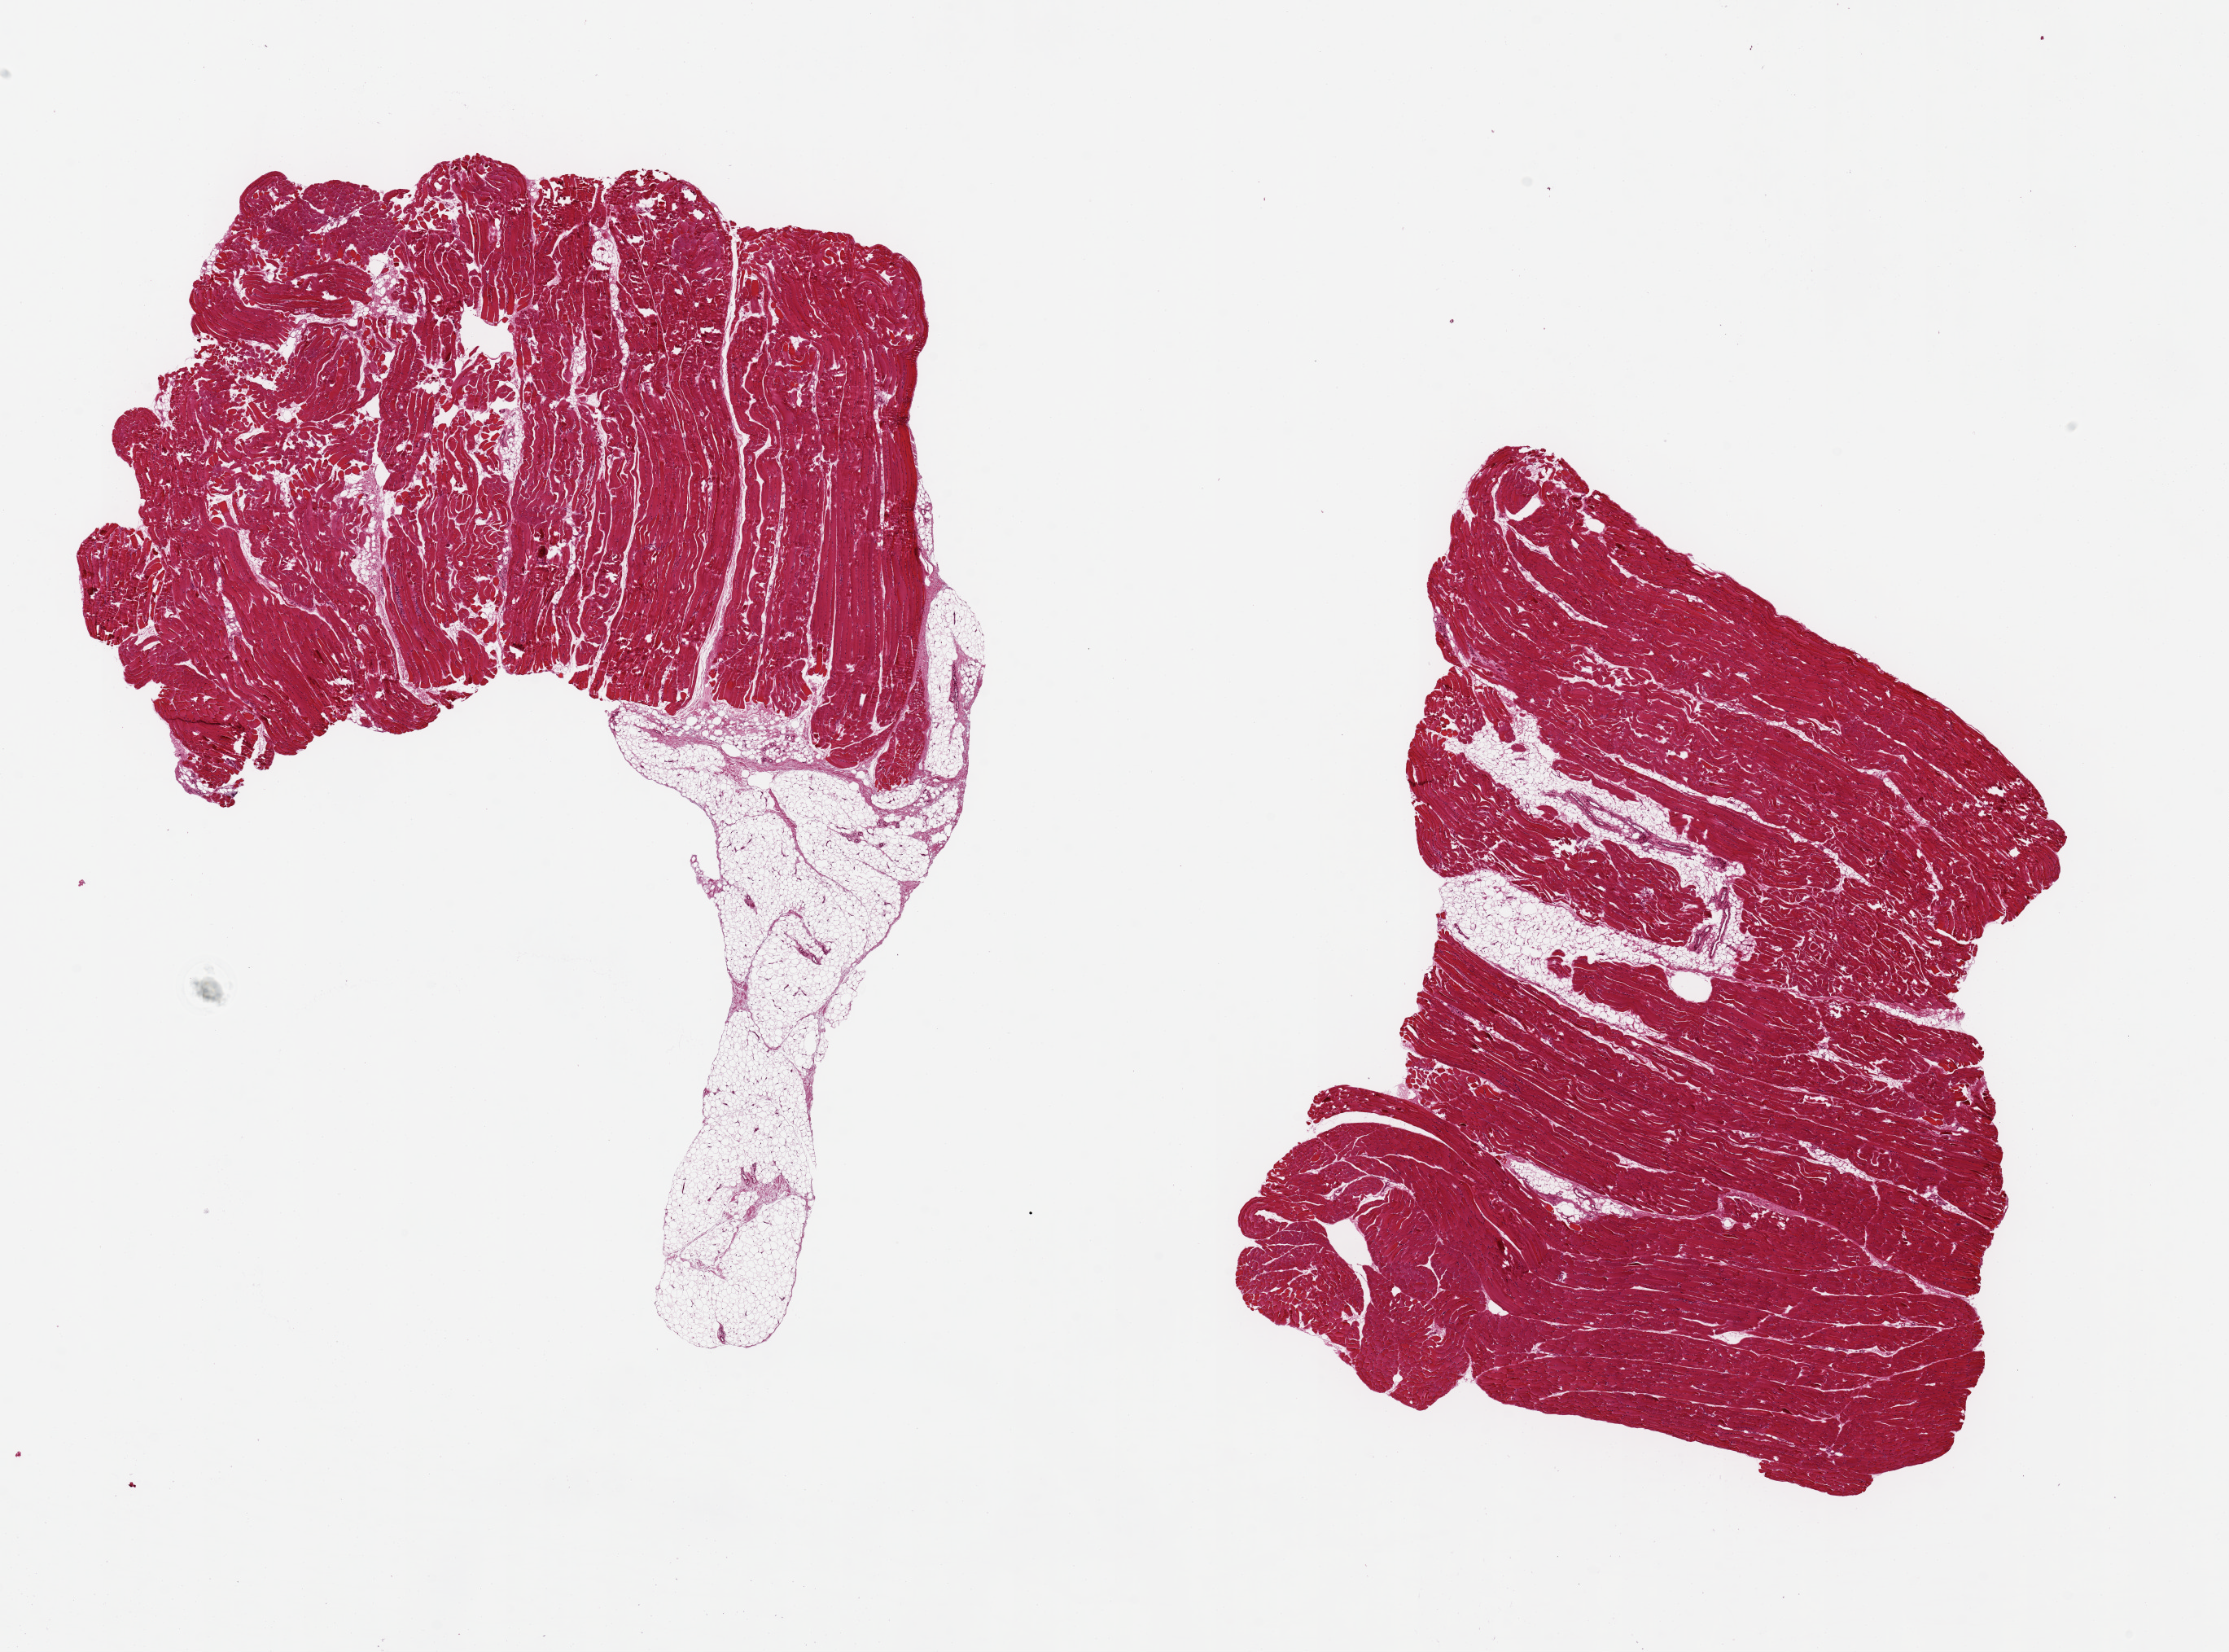
Digitized H&E-stained section, brightfield, a low-resolution overview of the entire scanned area, about 21.7 x 16.0 mm (from a 20x scan); PAXgene-fixed paraffin-embedded (PFPE) section; target tissue: skeletal muscle; donor tissue sample. Female donor.
Pathologist's review note for this sample: 2 pieces 9x7 & 8x5 mm; 5x2 mm adipose projection extends from one piece.